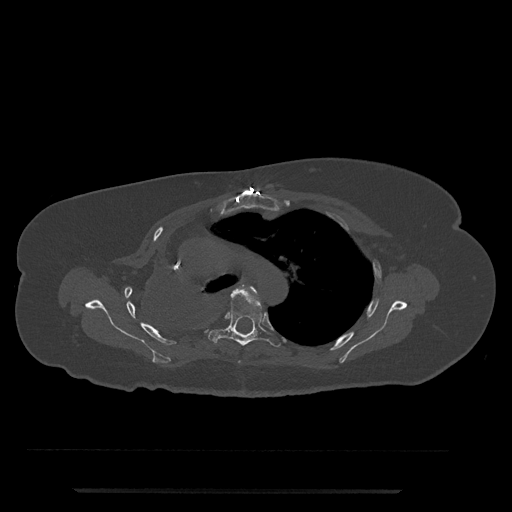
CT including the spine, one axial slice. Position 551 of 797 along the scan axis. 120 kVp. Bone window (W 1800 / L 400 HU). 0.5 mm slice thickness. 512 × 512 image matrix, field of view 440 × 440 mm. Female patient, age 51 years. From the clinical record (not read from this slice): primary cancer: neuro; vertebrae with lytic lesions (as recorded): T8.
Structures marked on this image (semi-automatically segmented with operator editing):
- T4 vertebra: box from (x=239, y=286) to (x=257, y=363) px
- T5 vertebra: (x=207, y=288)–(x=281, y=347)